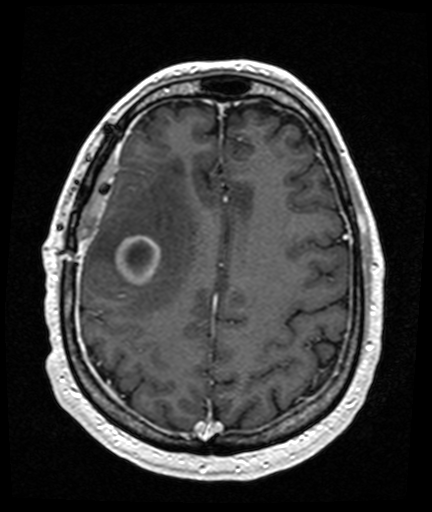
Brain MRI from a brain-tumour surgery series, one axial slice. Slice 51 of 176 in the series (ordered by position). T1-weighted post-contrast. 432 × 512 image matrix, field of view 194 × 230 mm. From the clinical record (not read from this slice): histopathology: Glioblastoma; WHO grade: 4; IDH mutation: no; tumour location: Right Frontal Temporal, Posterior Sylvian Fissure.
Structures marked on this image (outlined manually by an expert reader):
- tumour: box from (x=118, y=236) to (x=160, y=284) px